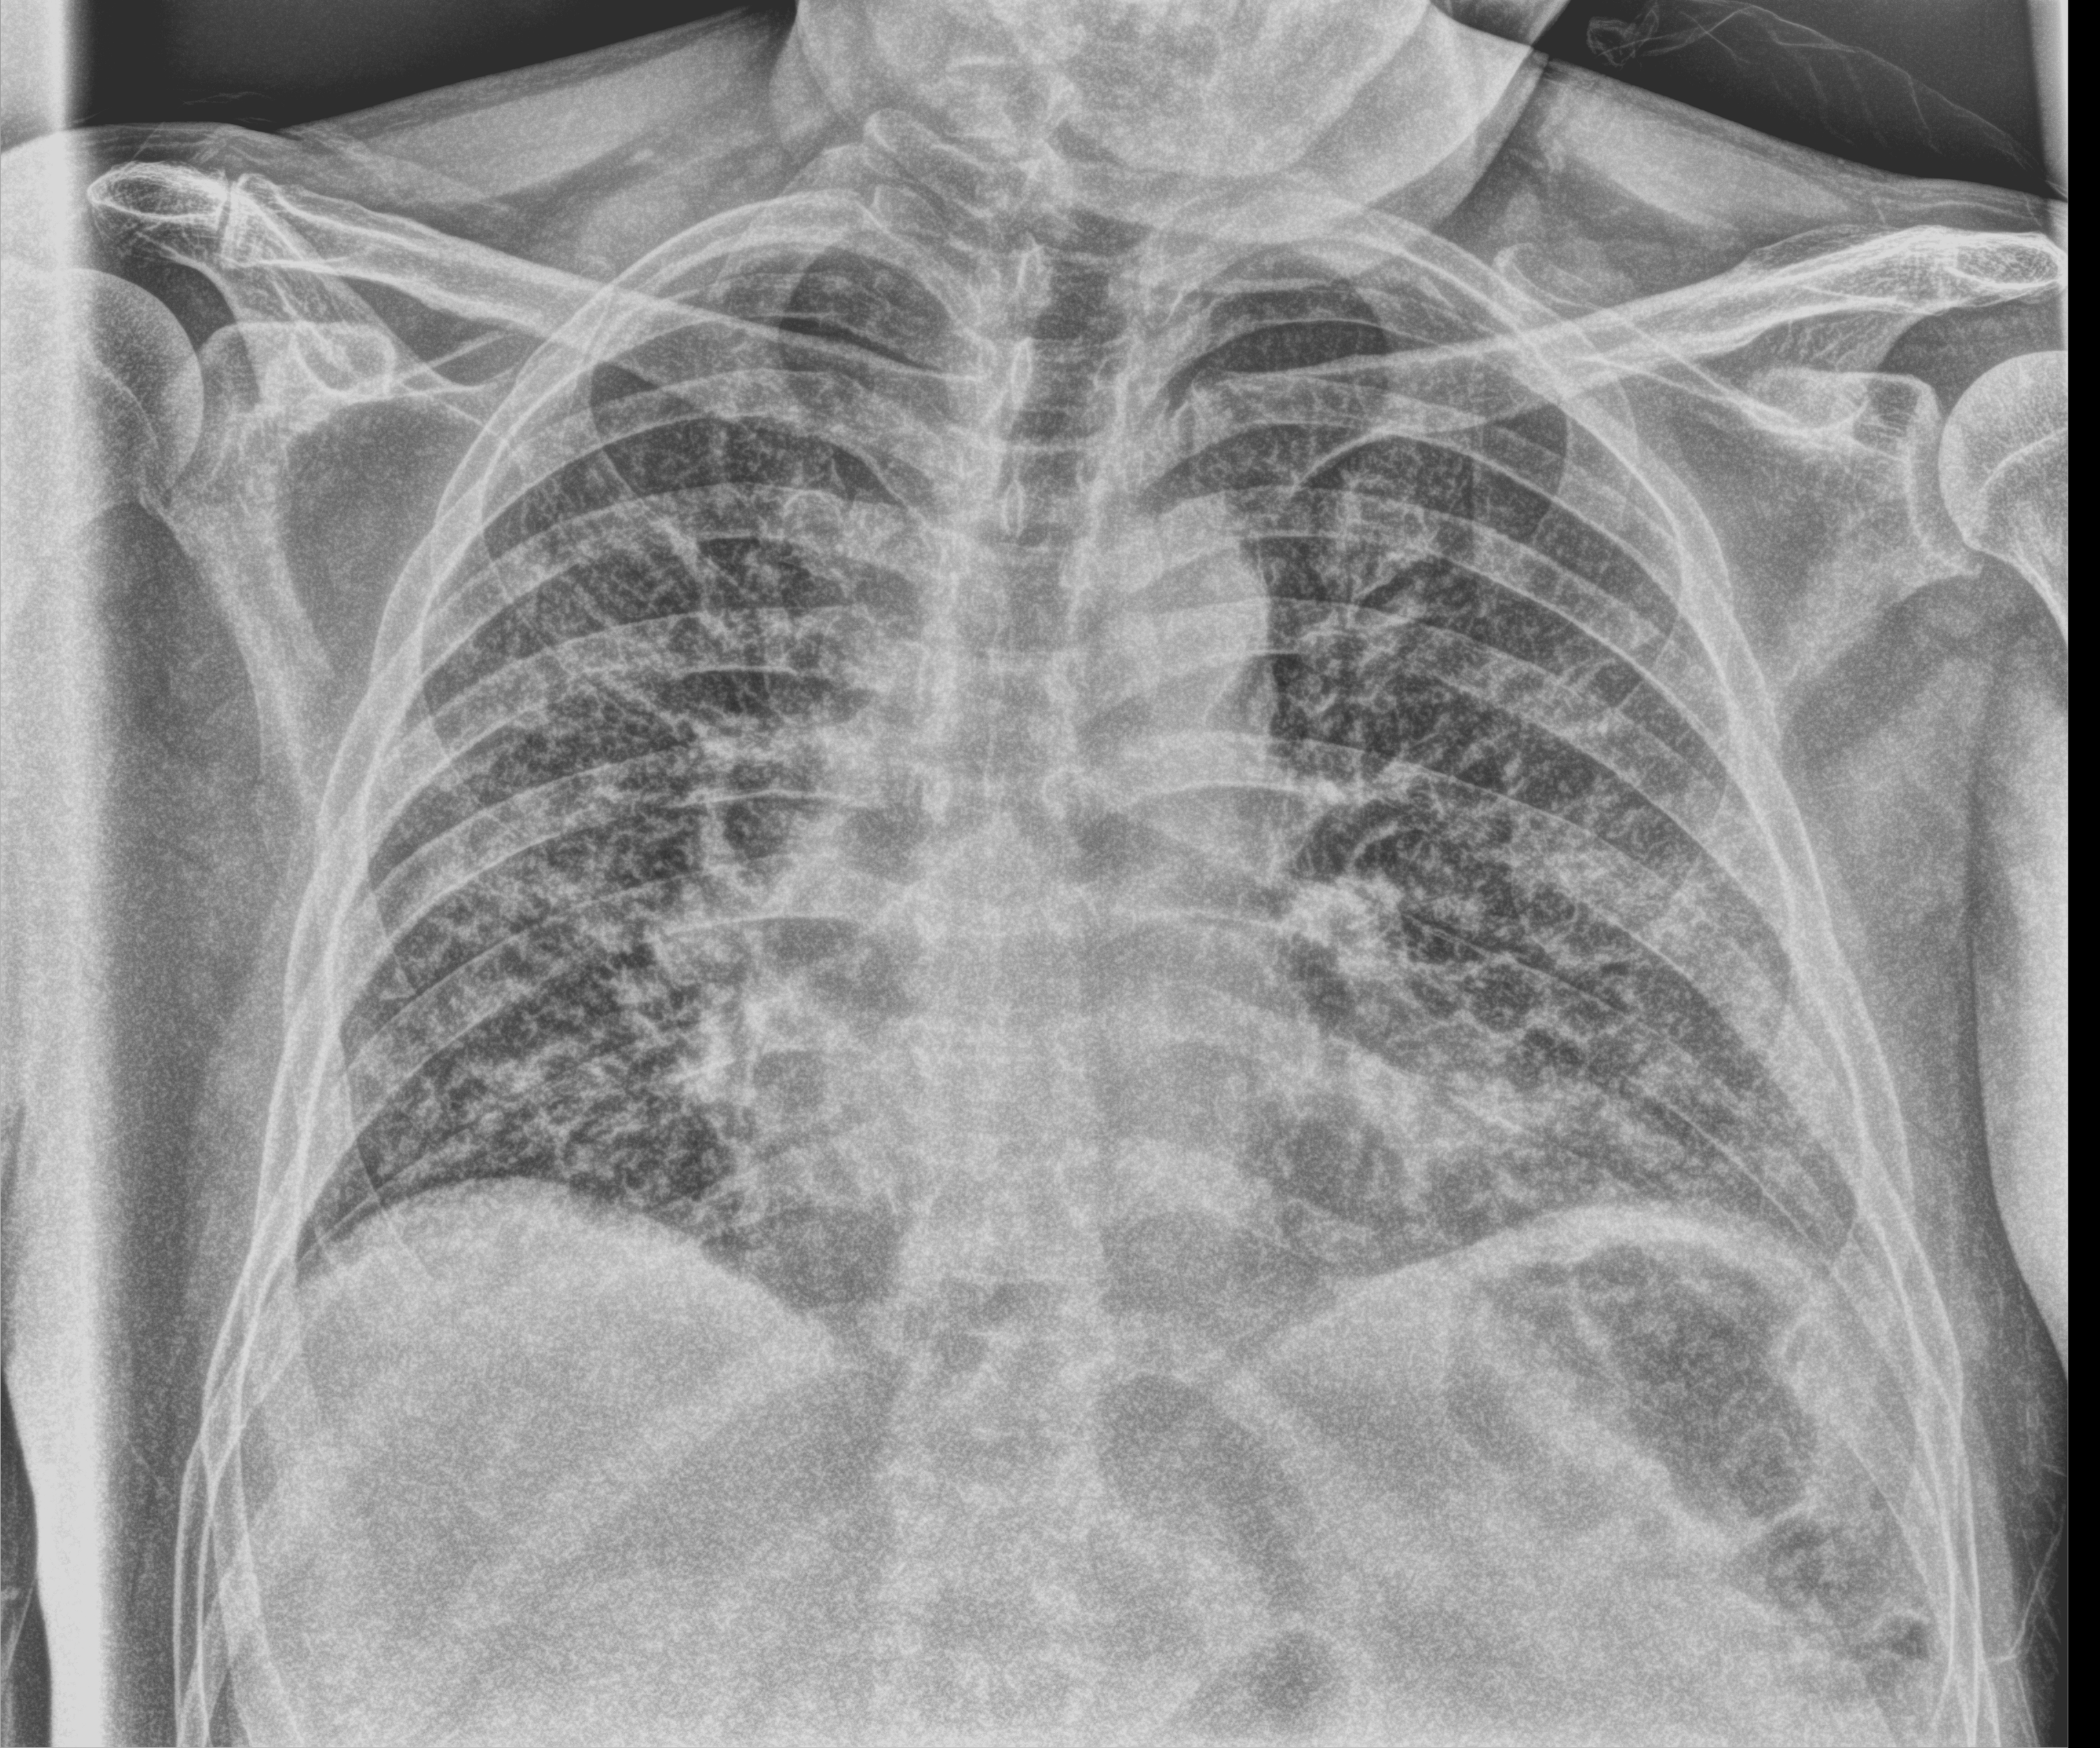
Chest X-ray (portable); anteroposterior (AP) projection. Male patient hospitalised with COVID-19, age 60–74 years.
Hospital-stay facts (about this admission, not read from this image; timing relative to this image not recorded): admitted to intensive care during this hospital stay: yes.